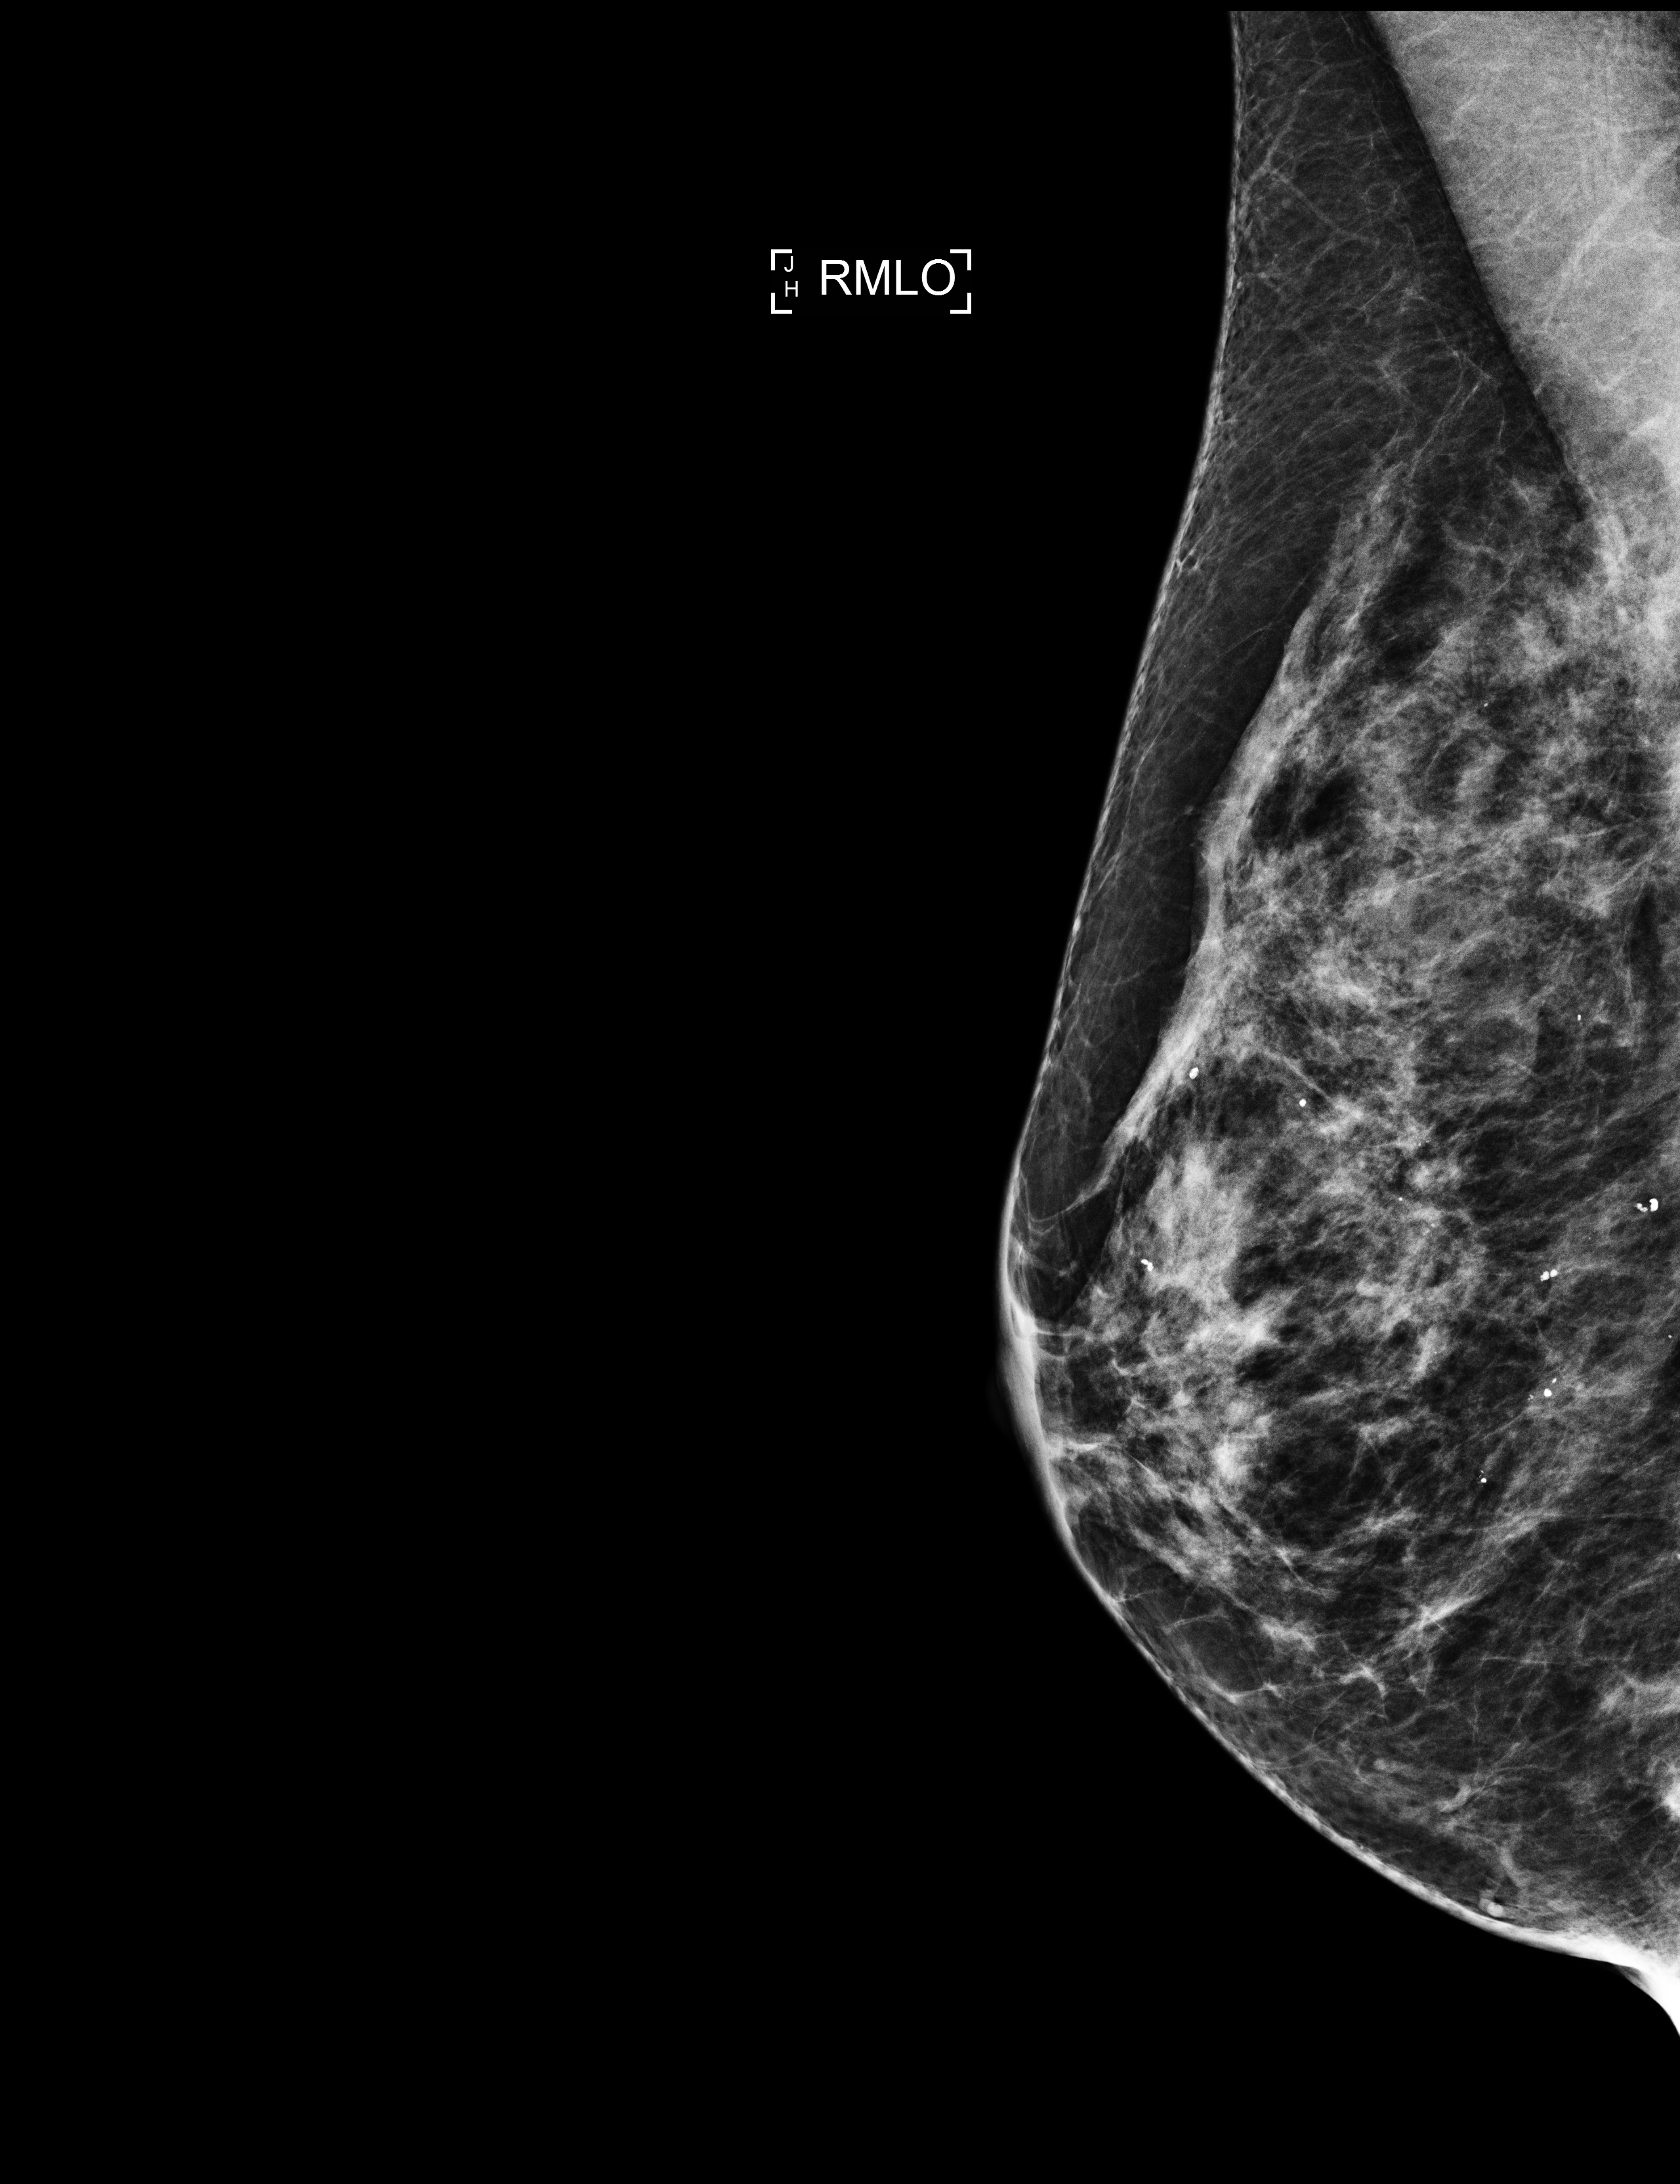
Full-field digital mammogram (FFDM), right breast, MLO view, annual screening mammography examination, compressed breast thickness 45 mm, system: Selenia Dimensions. Patient: female, 74 years.
BI-RADS breast density category at the screening exam (both breasts, scale 1–4): 3. Final BI-RADS category for the screening round (tomosynthesis exam, both breasts): category 2. Recall: no recall after this screen.